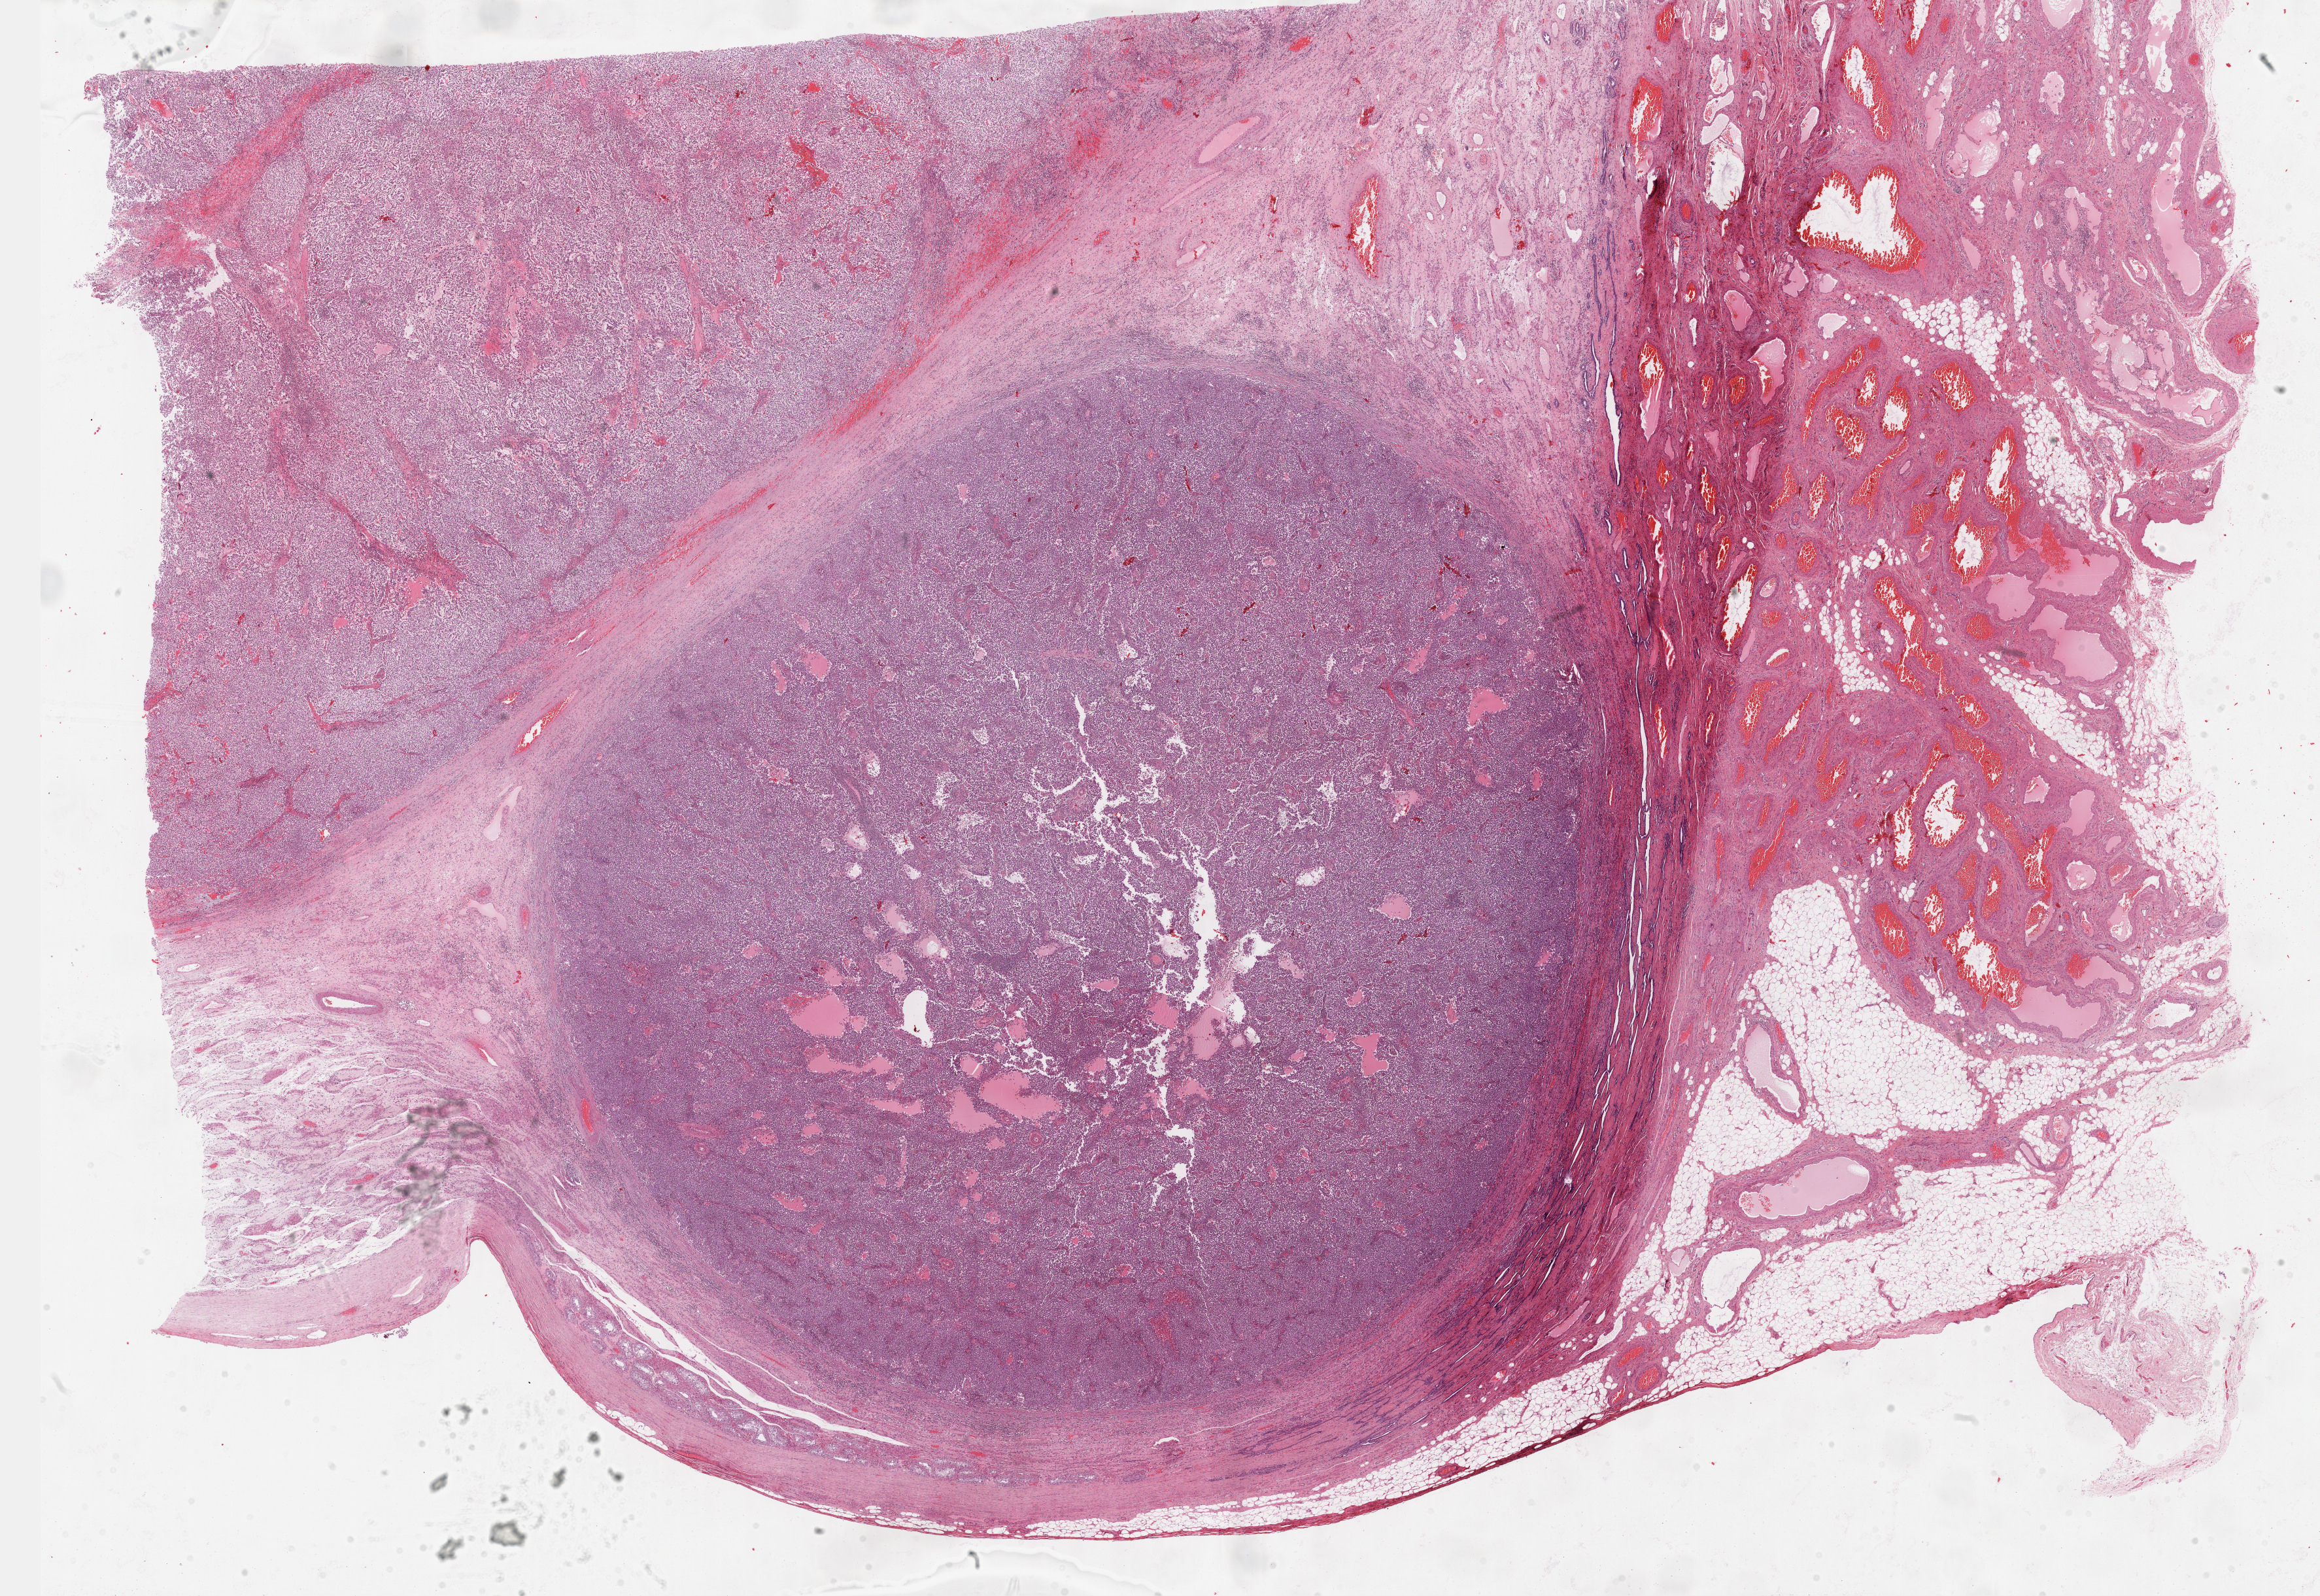
Whole-slide histology image, H&E-stained — shown as a low-resolution overview of the whole scanned area (about 28.7 x 19.7 mm, acquisition: 40x scan). Formalin-fixed paraffin-embedded (FFPE) diagnostic section. Sample: primary tumour, testis. Male patient; age at initial diagnosis 45 years.
AJCC pathologic stage: IB (7th edition). Pathologic diagnosis: Seminoma, NOS.